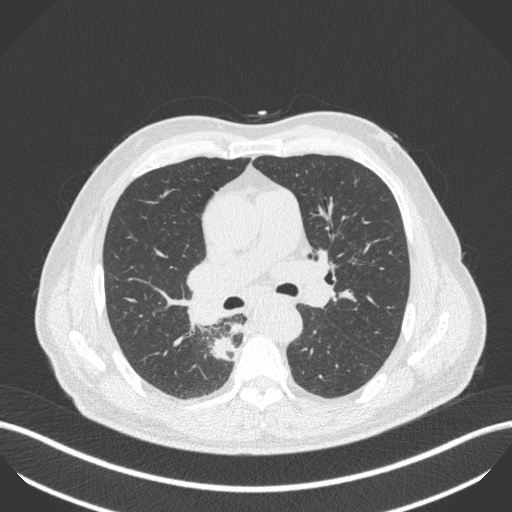
Chest CT, one axial slice; position 277 of 451 along the scan axis; reconstruction kernel B31f; 100 kVp; lung window (W 1500 / L -600 HU); 1 mm slice thickness; 512 × 512 image matrix, field of view 400 × 400 mm. Patient: male, 61 years. From the clinical record (not read from this slice): clinical TNM (as recorded): T1 N0 M0; histopathological grade: G3.
Structures marked on this image (bounding box drawn by a radiologist):
- lung tumour (recorded histology: small cell carcinoma): box from (x=208, y=335) to (x=239, y=363) px